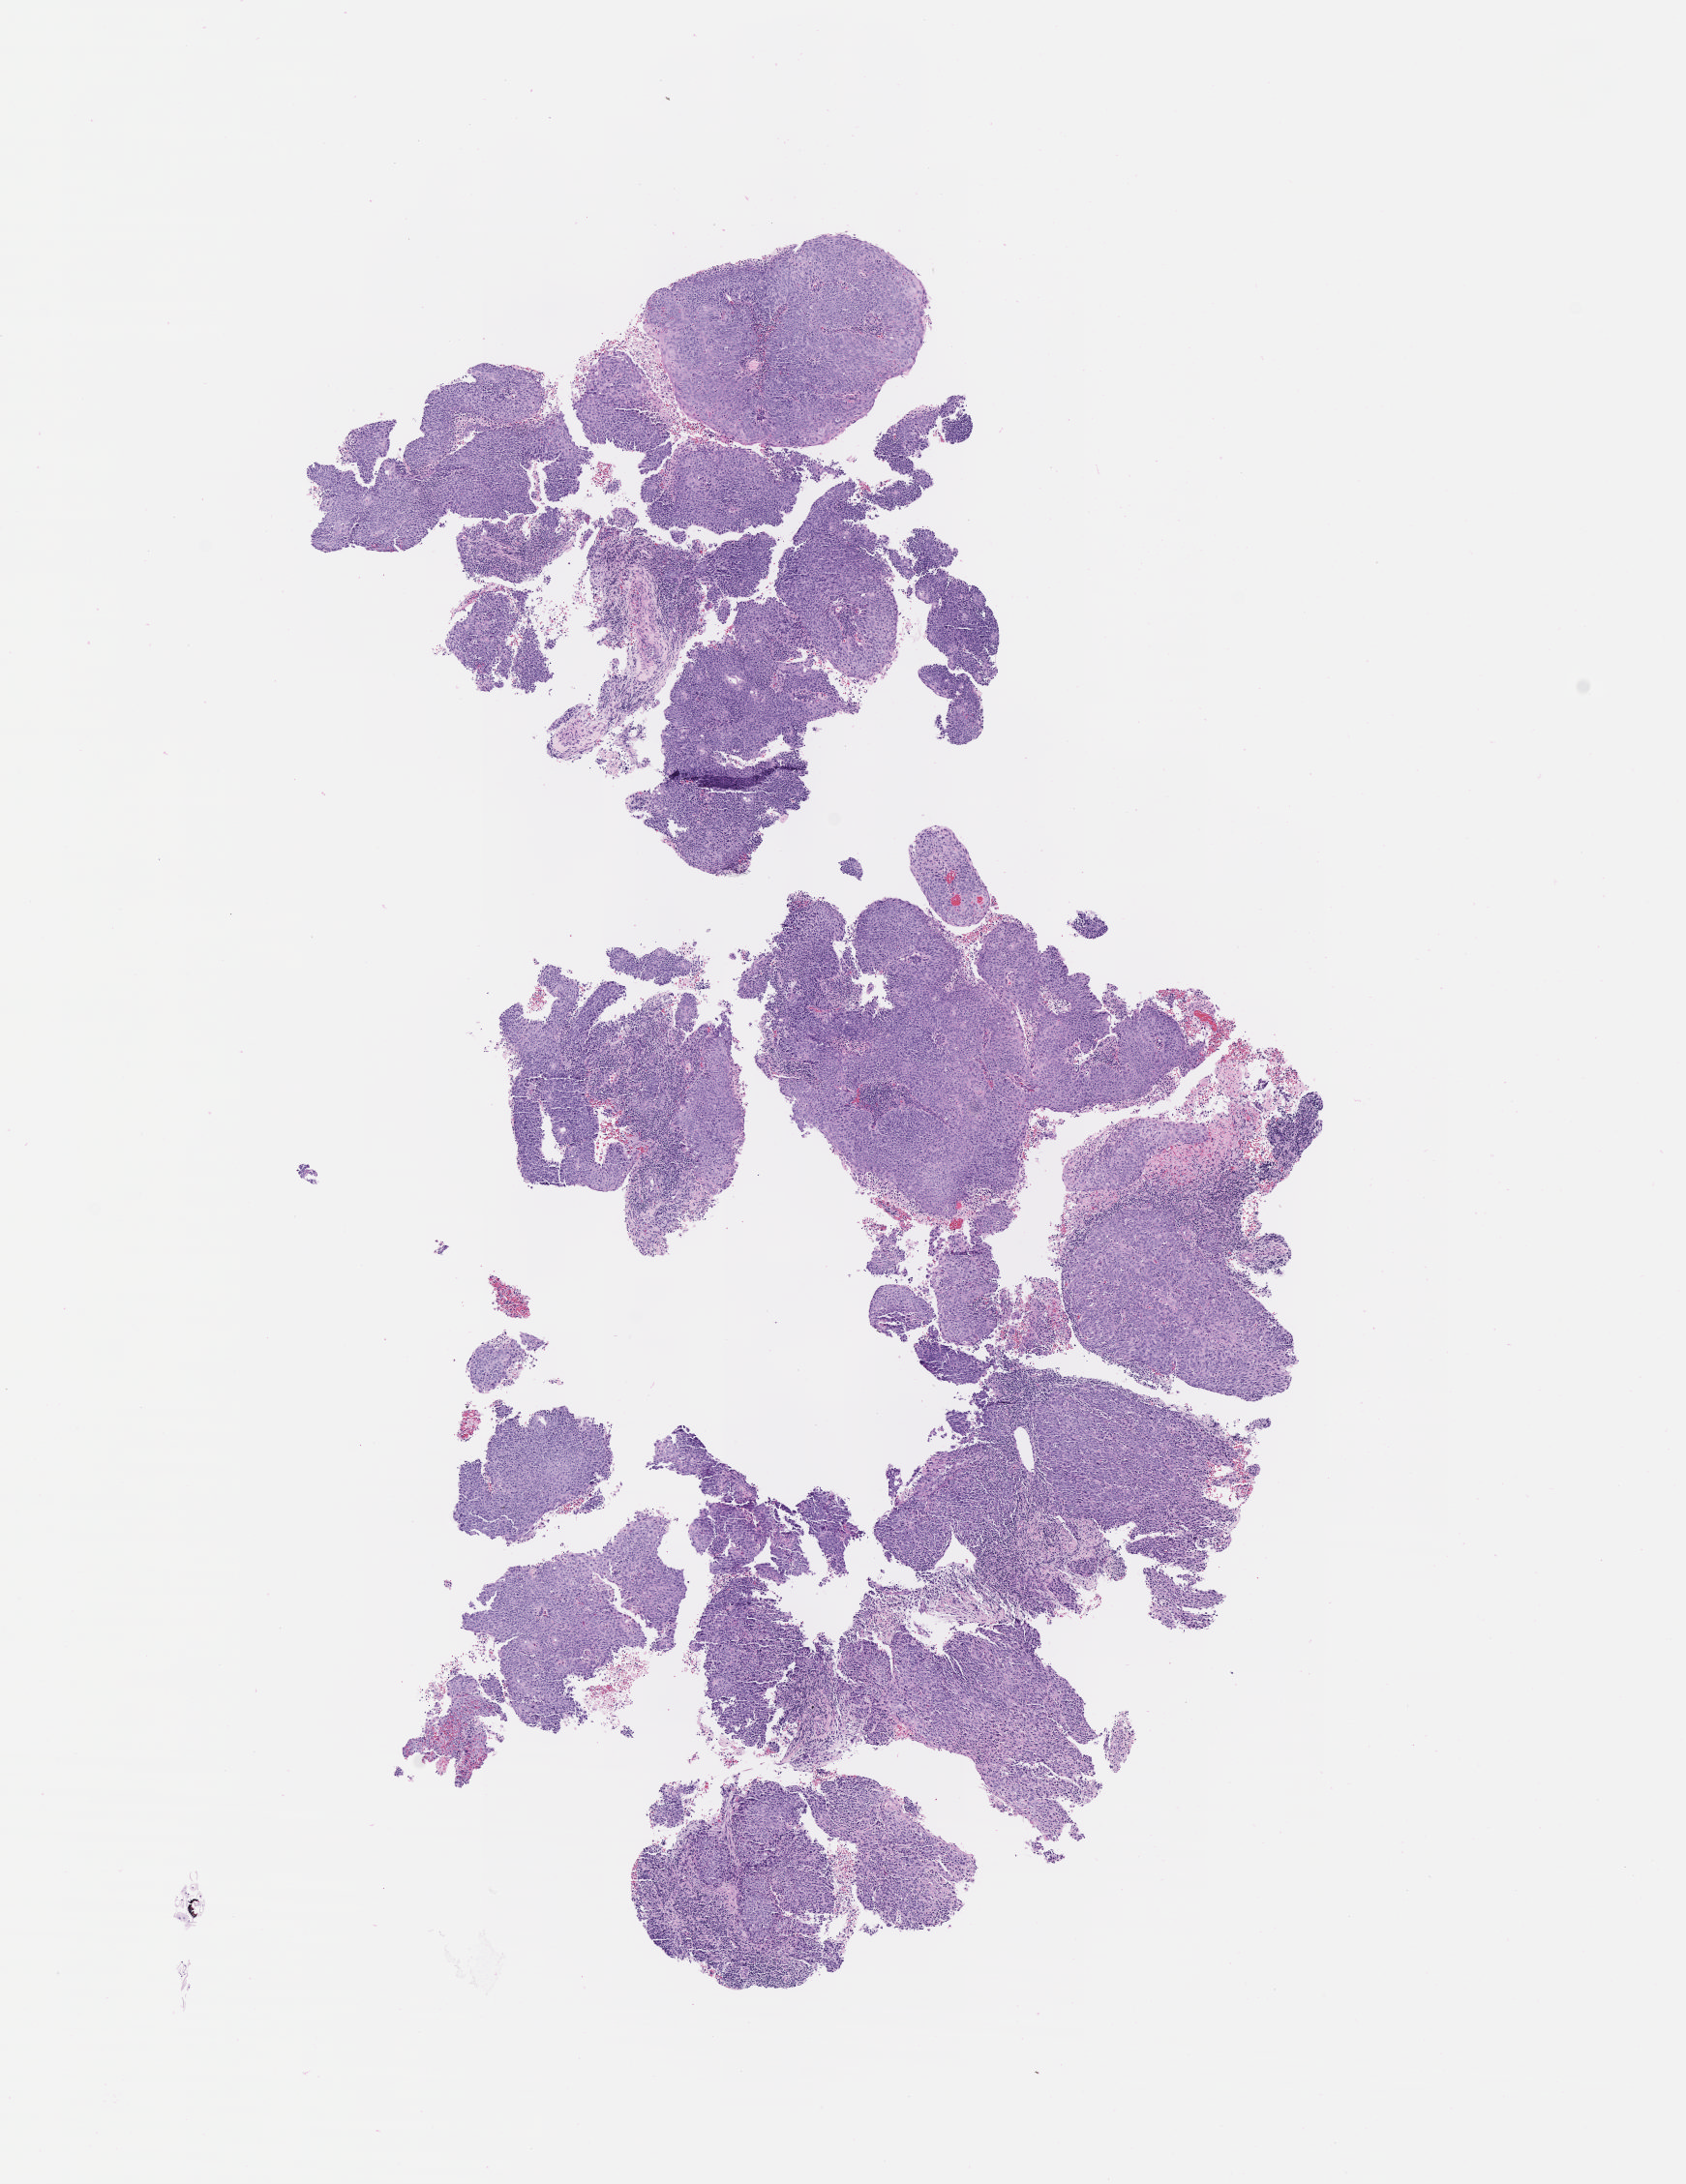
Whole-slide image, H&E stain, low-resolution overview of the scanned area, about 7.0 x 9.1 mm; tumor tissue; site: cervix. Female patient, 56 years old.
Diagnosis: Squamous cell carcinoma, large cell, nonkeratinizing, NOS.